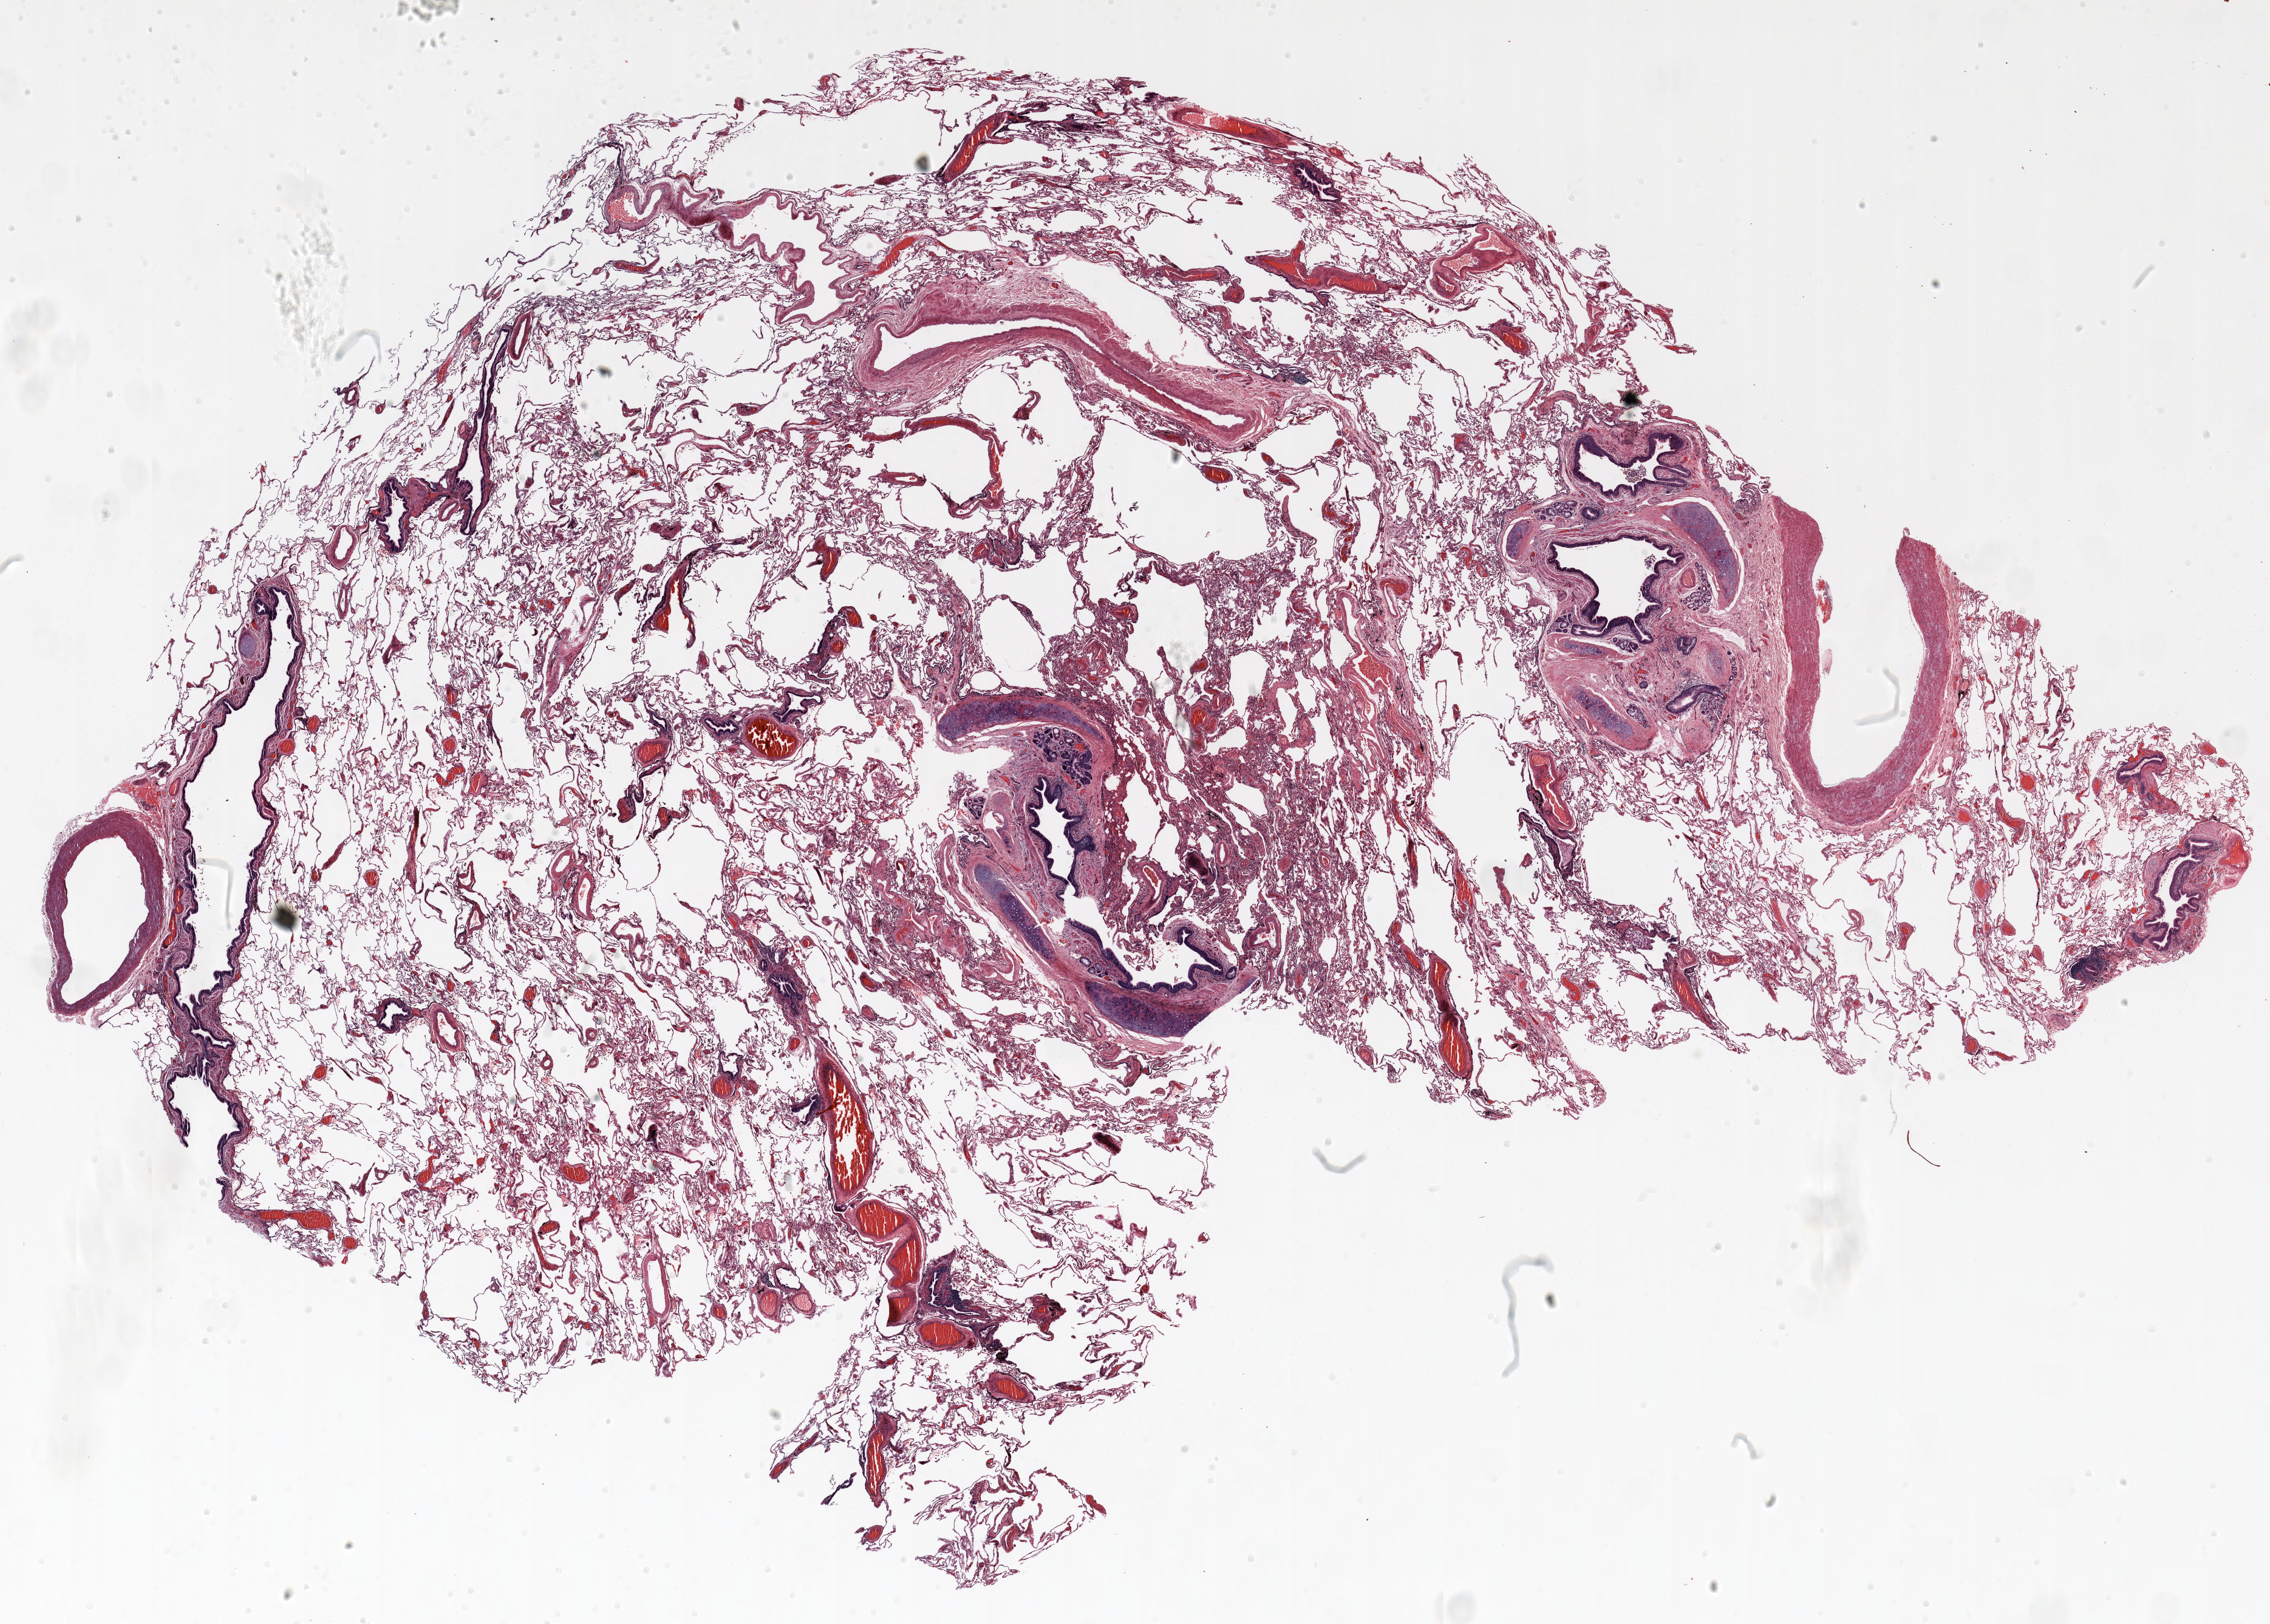
Hematoxylin and eosin (H&E) stained whole-slide image — shown as a low-resolution overview of the whole scanned area (about 30.0 x 21.5 mm). Formalin-fixed paraffin-embedded (FFPE) section. Lung tissue. Male patient, aged 66 at enrolment. Grade: poorly differentiated (G3).
• participant's lung-cancer diagnosis: Squamous cell carcinoma, NOS
• ICD-O-3 topography: upper lobe of lung (C34.1)
• tumour size (pathology): 15 mm
• stage (AJCC 6th edition): IA
• primary tumour location (clinical record): left upper lobe